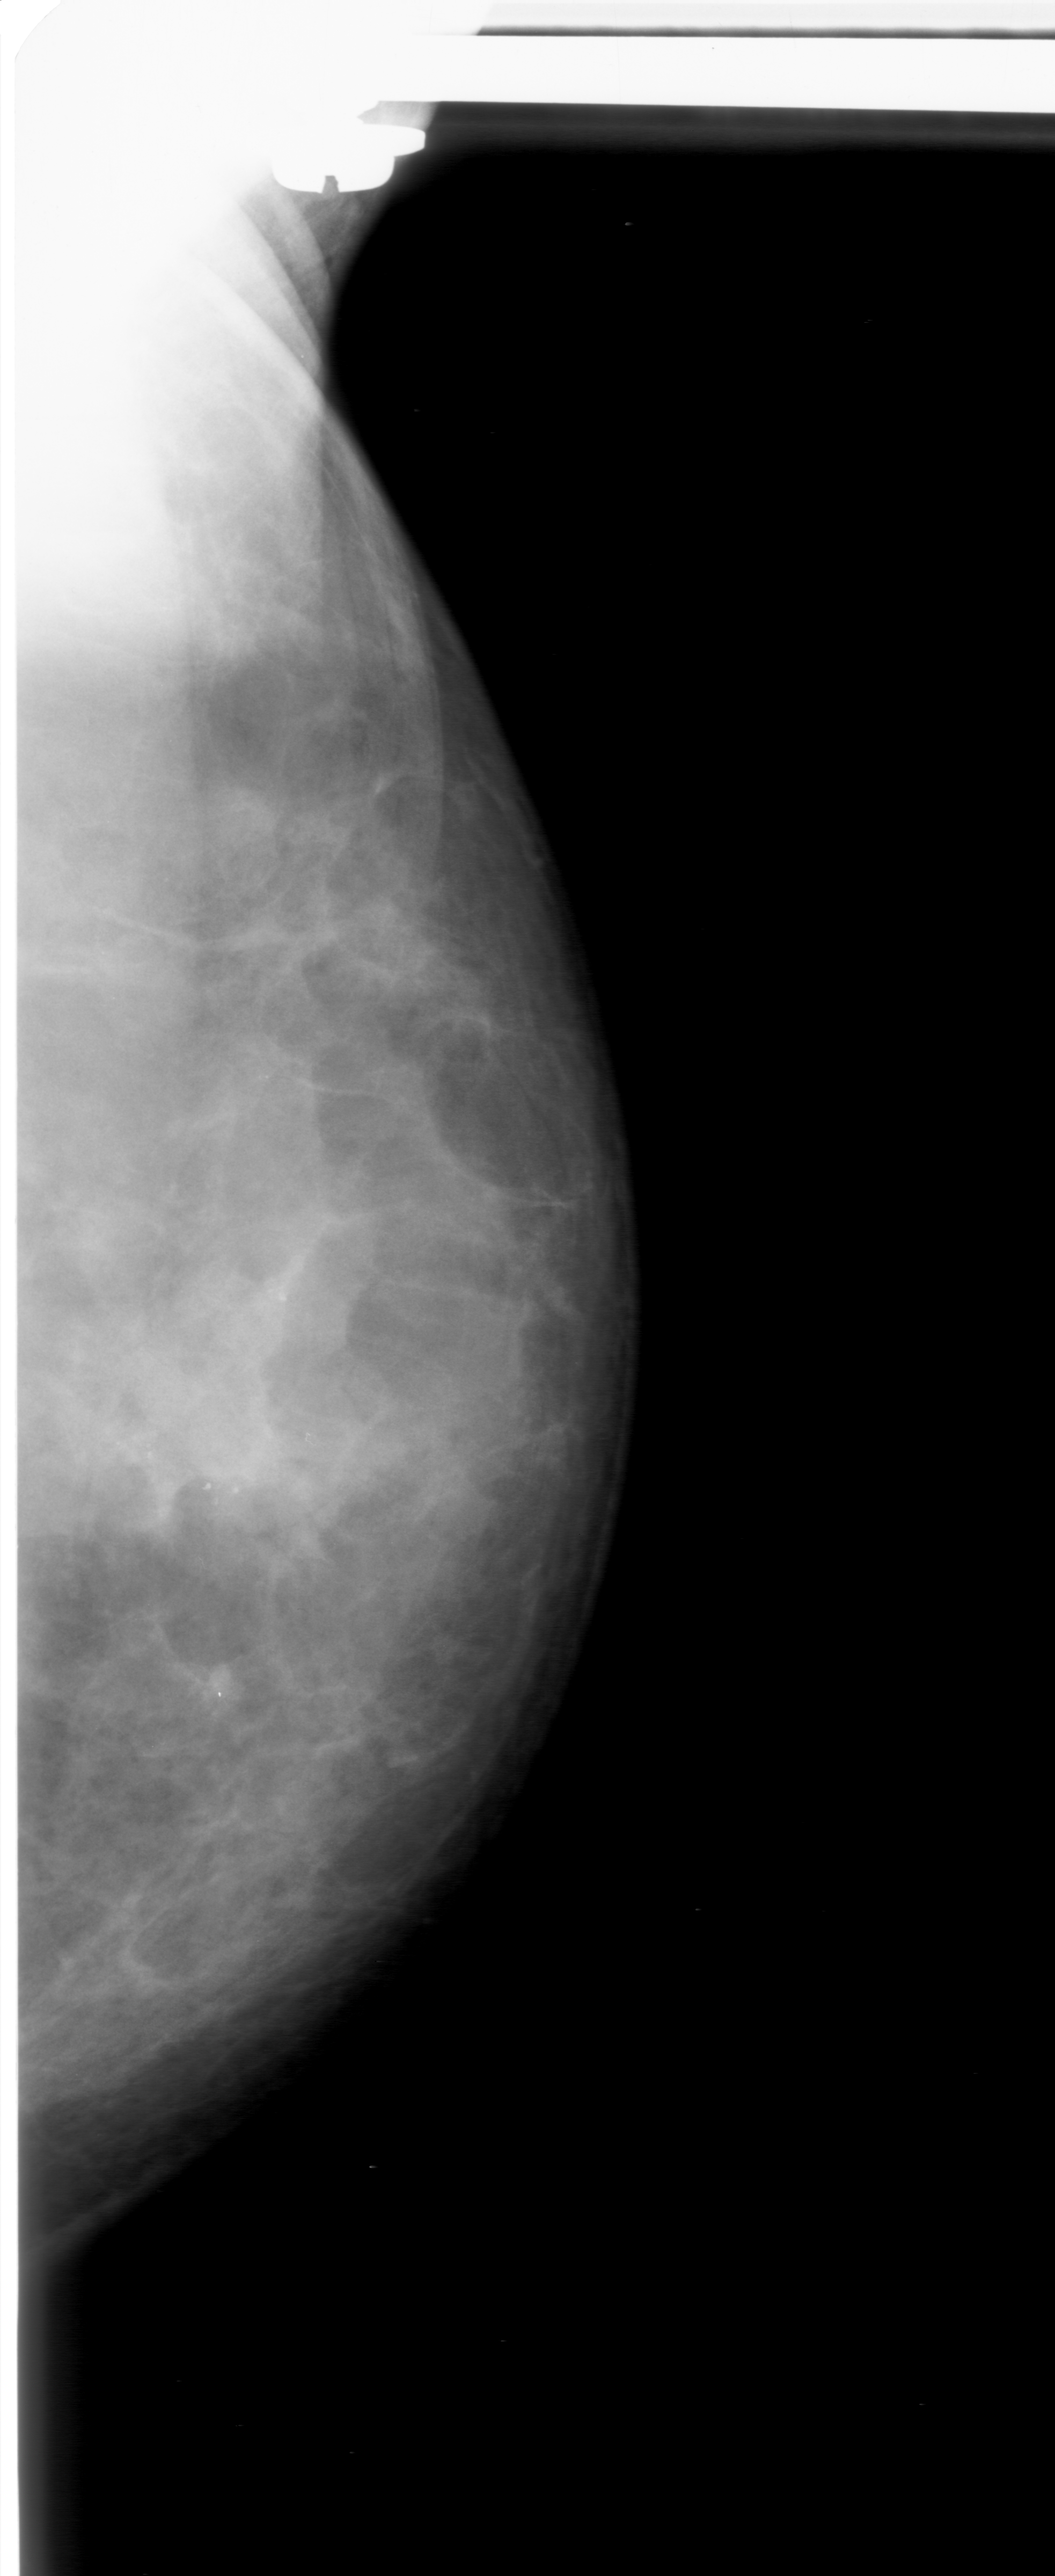
Scanned film-screen mammogram; left breast; CC view; BI-RADS breast density category 3 (scale 1–4).
Radiologist-marked abnormalities on this image: calcifications, morphology round and regular / pleomorphic, distribution clustered; BI-RADS assessment category 0 (incomplete: needs additional imaging); subtlety rating 3 on a 1 (subtle) to 5 (obvious) scale; pathology result (as recorded, not read from the image): benign.